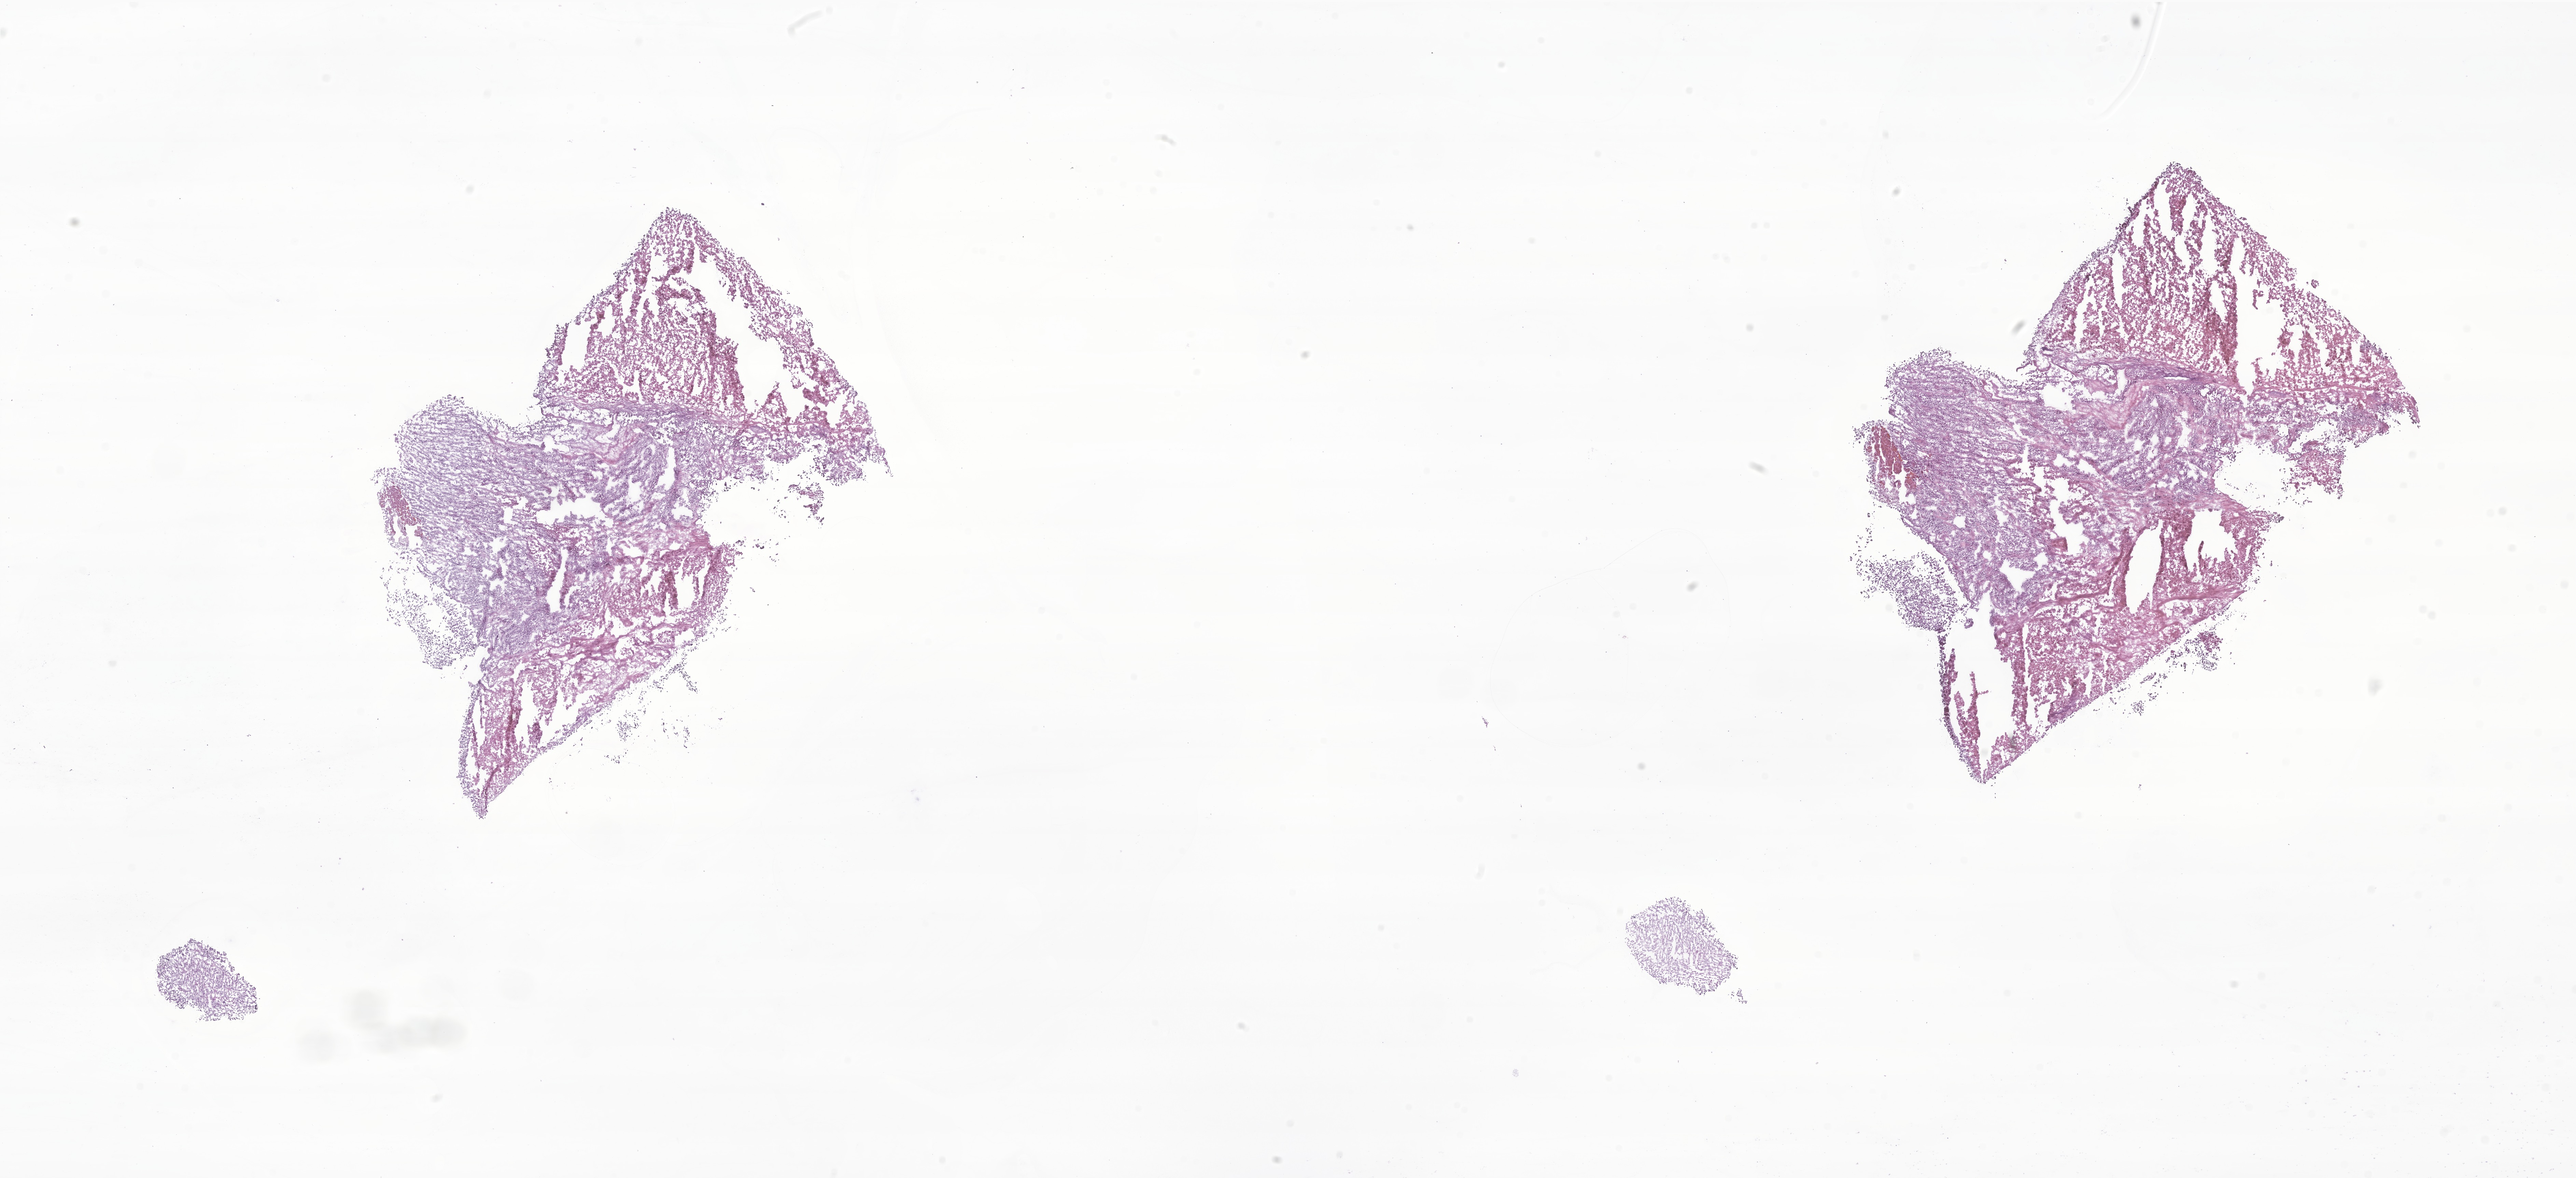
Hematoxylin and eosin (H&E) whole-slide image of tumor tissue from the adrenal gland — low-resolution overview of the scanned area, about 31.8 x 14.5 mm, frozen section. Female patient, age 174 months.
Recorded diagnosis: Adrenal cortical carcinoma.